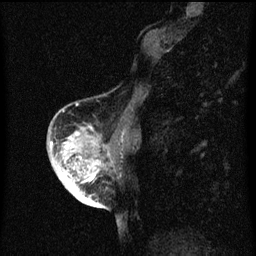
Breast MRI (dynamic contrast-enhanced), one sagittal slice. Position 23 of 60 along the scan axis. Dynamic contrast-enhanced series, image 2 of 3 at this slice position (ordered by acquisition). 1.5 T. TE 4.2 ms, TR 8 ms. 256 × 256 image matrix. Patient: female, 56 years.
Annotated regions visible in this slice (semi-automatically segmented with operator editing):
- analysis volume of interest (the breast-tissue region the enhancement analysis was run in; not a lesion): bounding box [x1, y1, x2, y2] px = [54, 122, 118, 199]
- tumour enhancement mask (voxels above the 70 % enhancement threshold inside the analysis volume of interest): [59, 132, 101, 199]